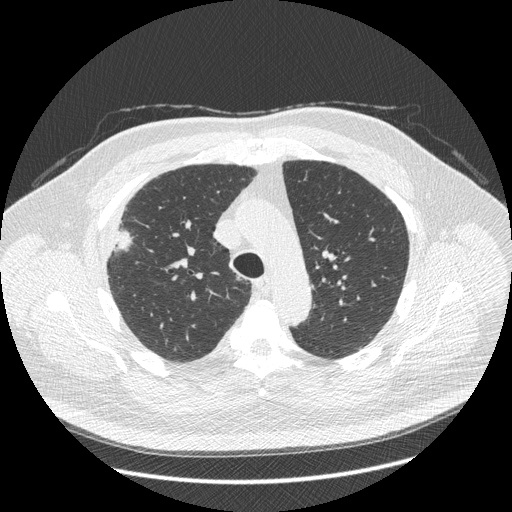
Low-dose screening chest CT, one axial slice; position 312 of 426 along the scan axis; lung window (W 1500 / L -600 HU); 1.25 mm slice thickness; 512 × 512 image matrix, field of view 400 × 400 mm.
Annotated regions visible in this slice (expert manual segmentation):
- lesion 1 (tumor, upper lobe of right lung): bounding box (x1, y1, x2, y2) in pixels: (116, 231, 132, 250)